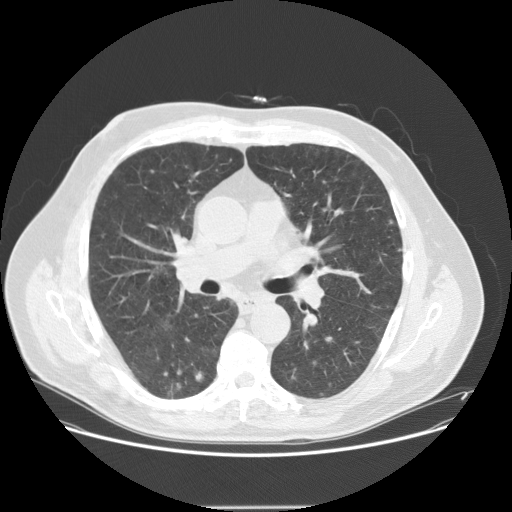
Low-dose screening chest CT, one axial slice. Position 84 of 143 along the scan axis. Reconstruction kernel STANDARD. Lung window (W 1500 / L -600 HU). 2.5 mm slice thickness. 512 × 512 image matrix, field of view 400 × 400 mm.
Structures marked on this image (outlined manually by an expert reader):
- lesion 4 (tumor, lower lobe of right lung): bounding box (x1, y1, x2, y2) in pixels: (195, 372, 203, 382)